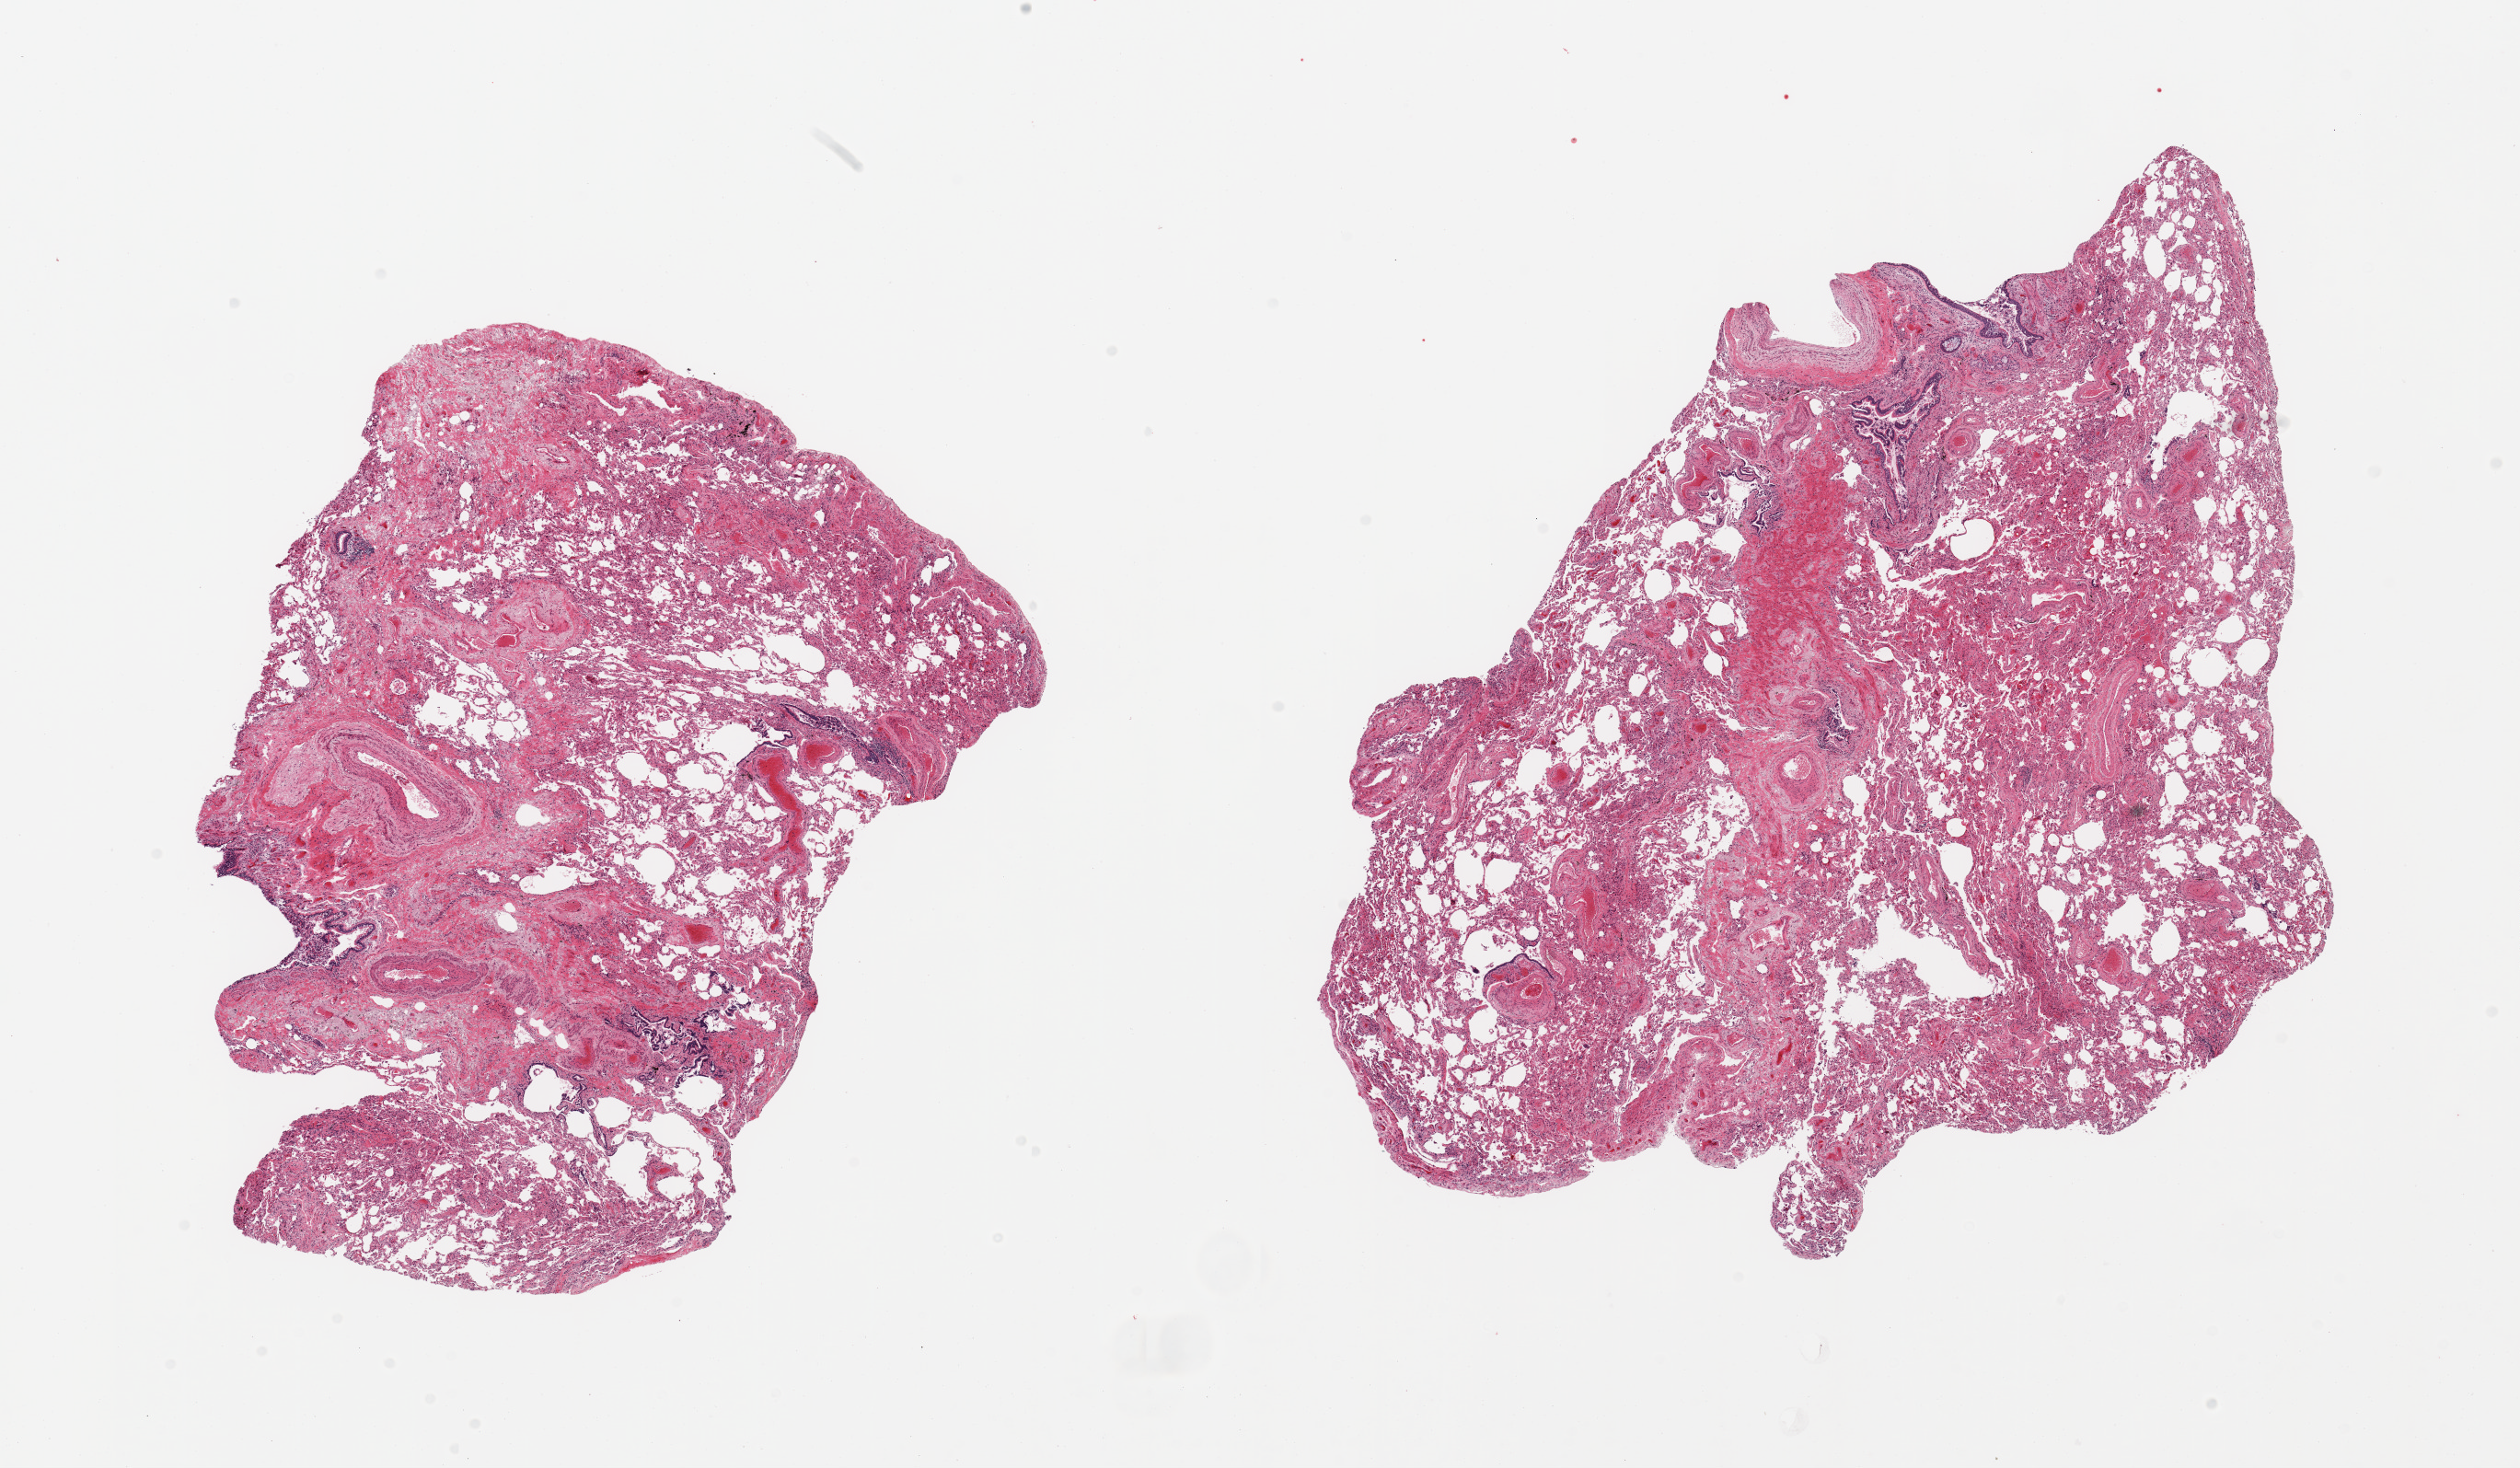
Whole-slide image, hematoxylin and eosin (H&E) stain, low-resolution overview of the scanned area, about 21.7 x 12.6 mm; PAXgene-fixed paraffin-embedded (PFPE) section; target tissue: lung; tissue donor sample. Donor: female.
Reviewer comment on this tissue sample: 2 pieces, moderate congestion/atalectasis.